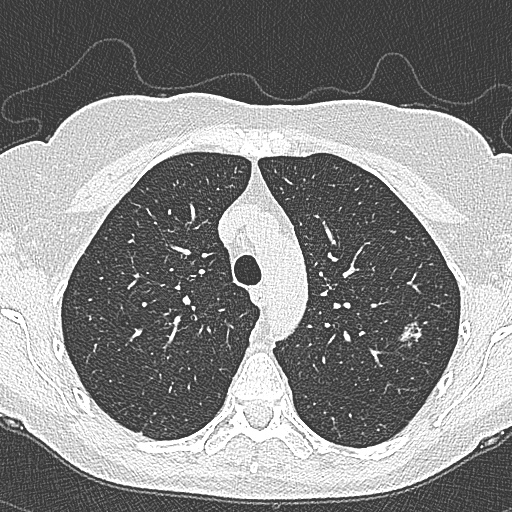
Axial slice from a low-dose chest CT screening exam, second annual screen, lung window (W 1500 / L -600 HU), lung (sharp) reconstruction kernel (B80f), 512 × 512 image matrix. Female participant, aged 65 years at enrolment.
• Expert reader's lesion annotation, bounding box <395,311,443,359> (left, top, right, bottom; pixels).
• The screening reader recorded 4 non-calcified nodules or masses ≥4 mm on this exam (left upper lobe, left upper lobe, left upper lobe, right lower lobe); which of them this box marks is not recorded.
• Official screen result: positive, change unspecified: nodule(s) >= 4 mm or enlarging nodule(s), mass(es), or other non-specific abnormalities suspicious for lung cancer.